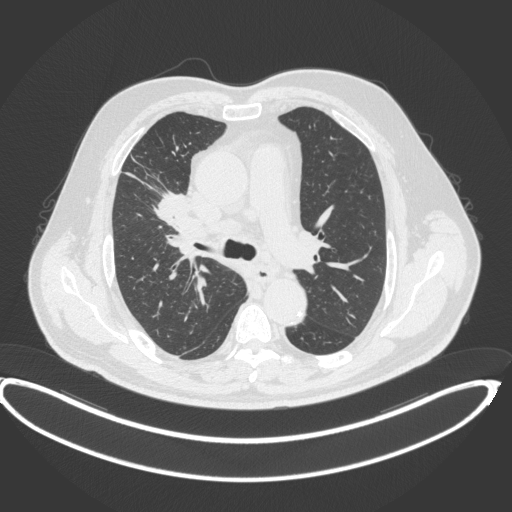
Chest CT, one axial slice; slice 267 of 395 in the series (ordered by position); 120 kVp; lung window (W 1500 / L -600 HU); 1 mm slice thickness; 512 × 512 image matrix, field of view 448 × 448 mm. Male patient, age 62 years. Case-level facts recorded for this patient, not image findings: clinical TNM (as recorded): T1c N3 M1c.
Structures marked on this image (rectangle marked by the reading radiologist):
- lung tumour (recorded histology: adenocarcinoma): bounding box <153,186,193,228> (left, top, right, bottom; pixels)